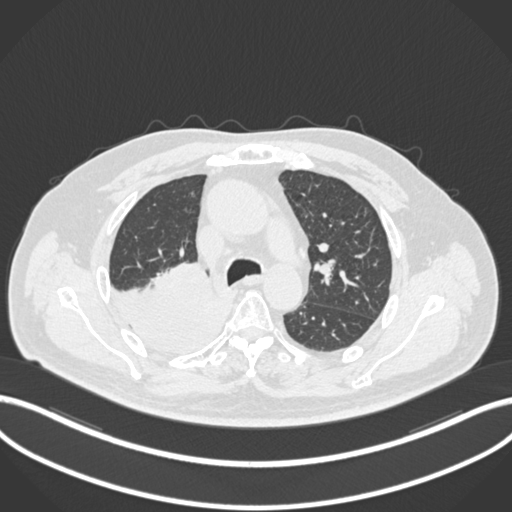
Chest CT, one axial slice; position 137 of 218 along the scan axis; reconstruction kernel B30f; lung window (W 1500 / L -600 HU); 1 mm slice thickness; 512 × 512 image matrix, field of view 400 × 400 mm. Patient: male, 68 years. Case-level facts recorded for this patient, not image findings: clinical TNM (as recorded): T2a N0 M0.
Annotated regions visible in this slice (rectangle marked by the reading radiologist):
- lung tumour (recorded histology: adenocarcinoma): box from (x=113, y=264) to (x=227, y=357) px